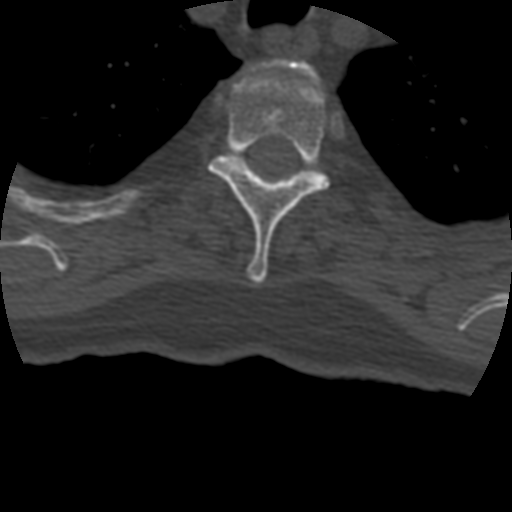
CT including the spine, one axial slice. Slice 352 of 399 in the series (ordered by position). Bone window (W 1800 / L 400 HU). 1.25 mm slice thickness. 512 × 512 image matrix, field of view 160 × 160 mm. Patient age 69 years. From the clinical record (not read from this slice): primary cancer: prostate.
Structures marked on this image (semi-automatic segmentation, software-assisted and operator-edited):
- T2 vertebra: bounding box [x1, y1, x2, y2] px = [291, 63, 310, 74]
- T3 vertebra: [209, 65, 330, 284]
- T4 vertebra: [182, 156, 309, 208]